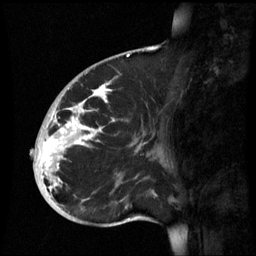
Breast MRI (dynamic contrast-enhanced), one sagittal slice. Position 24 of 60 along the scan axis. Dynamic contrast-enhanced series, image 2 of 3 at this slice position (ordered by acquisition). 1.5 T. TE 4.2 ms, TR 8.9 ms. 2.6 mm slice thickness. 256 × 256 image matrix. Patient: female, 35 years. From the clinical record (not read from this slice): setting: breast cancer imaged before/during neoadjuvant chemotherapy; receptor status: HR-positive, HER2-negative.
Annotated regions visible in this slice (semi-automatically segmented with operator editing):
- analysis volume of interest (the breast-tissue region the enhancement analysis was run in; not a lesion): box from (x=32, y=74) to (x=164, y=221) px
- tumour enhancement mask (voxels above the 70 % enhancement threshold inside the analysis volume of interest): (x=39, y=84)–(x=114, y=191)